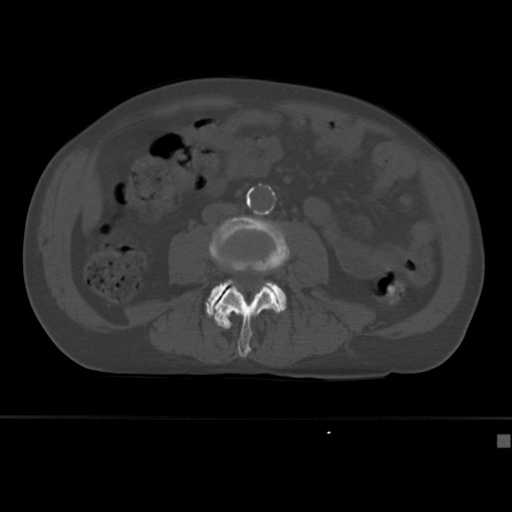
CT including the spine, one axial slice. Position 119 of 430 along the scan axis. Bone window (W 1800 / L 400 HU). 1.5 mm slice thickness. 512 × 512 image matrix. Male patient, age 64 years. From the clinical record (not read from this slice): primary cancer: uterus; vertebrae with lytic lesions (as recorded): T1, T4, T5, T7, L5.
Outlined on this slice (semi-automatic segmentation, software-assisted and operator-edited):
- L3 vertebra: bounding box [x1, y1, x2, y2] px = [208, 215, 290, 357]
- L4 vertebra: [205, 280, 287, 329]